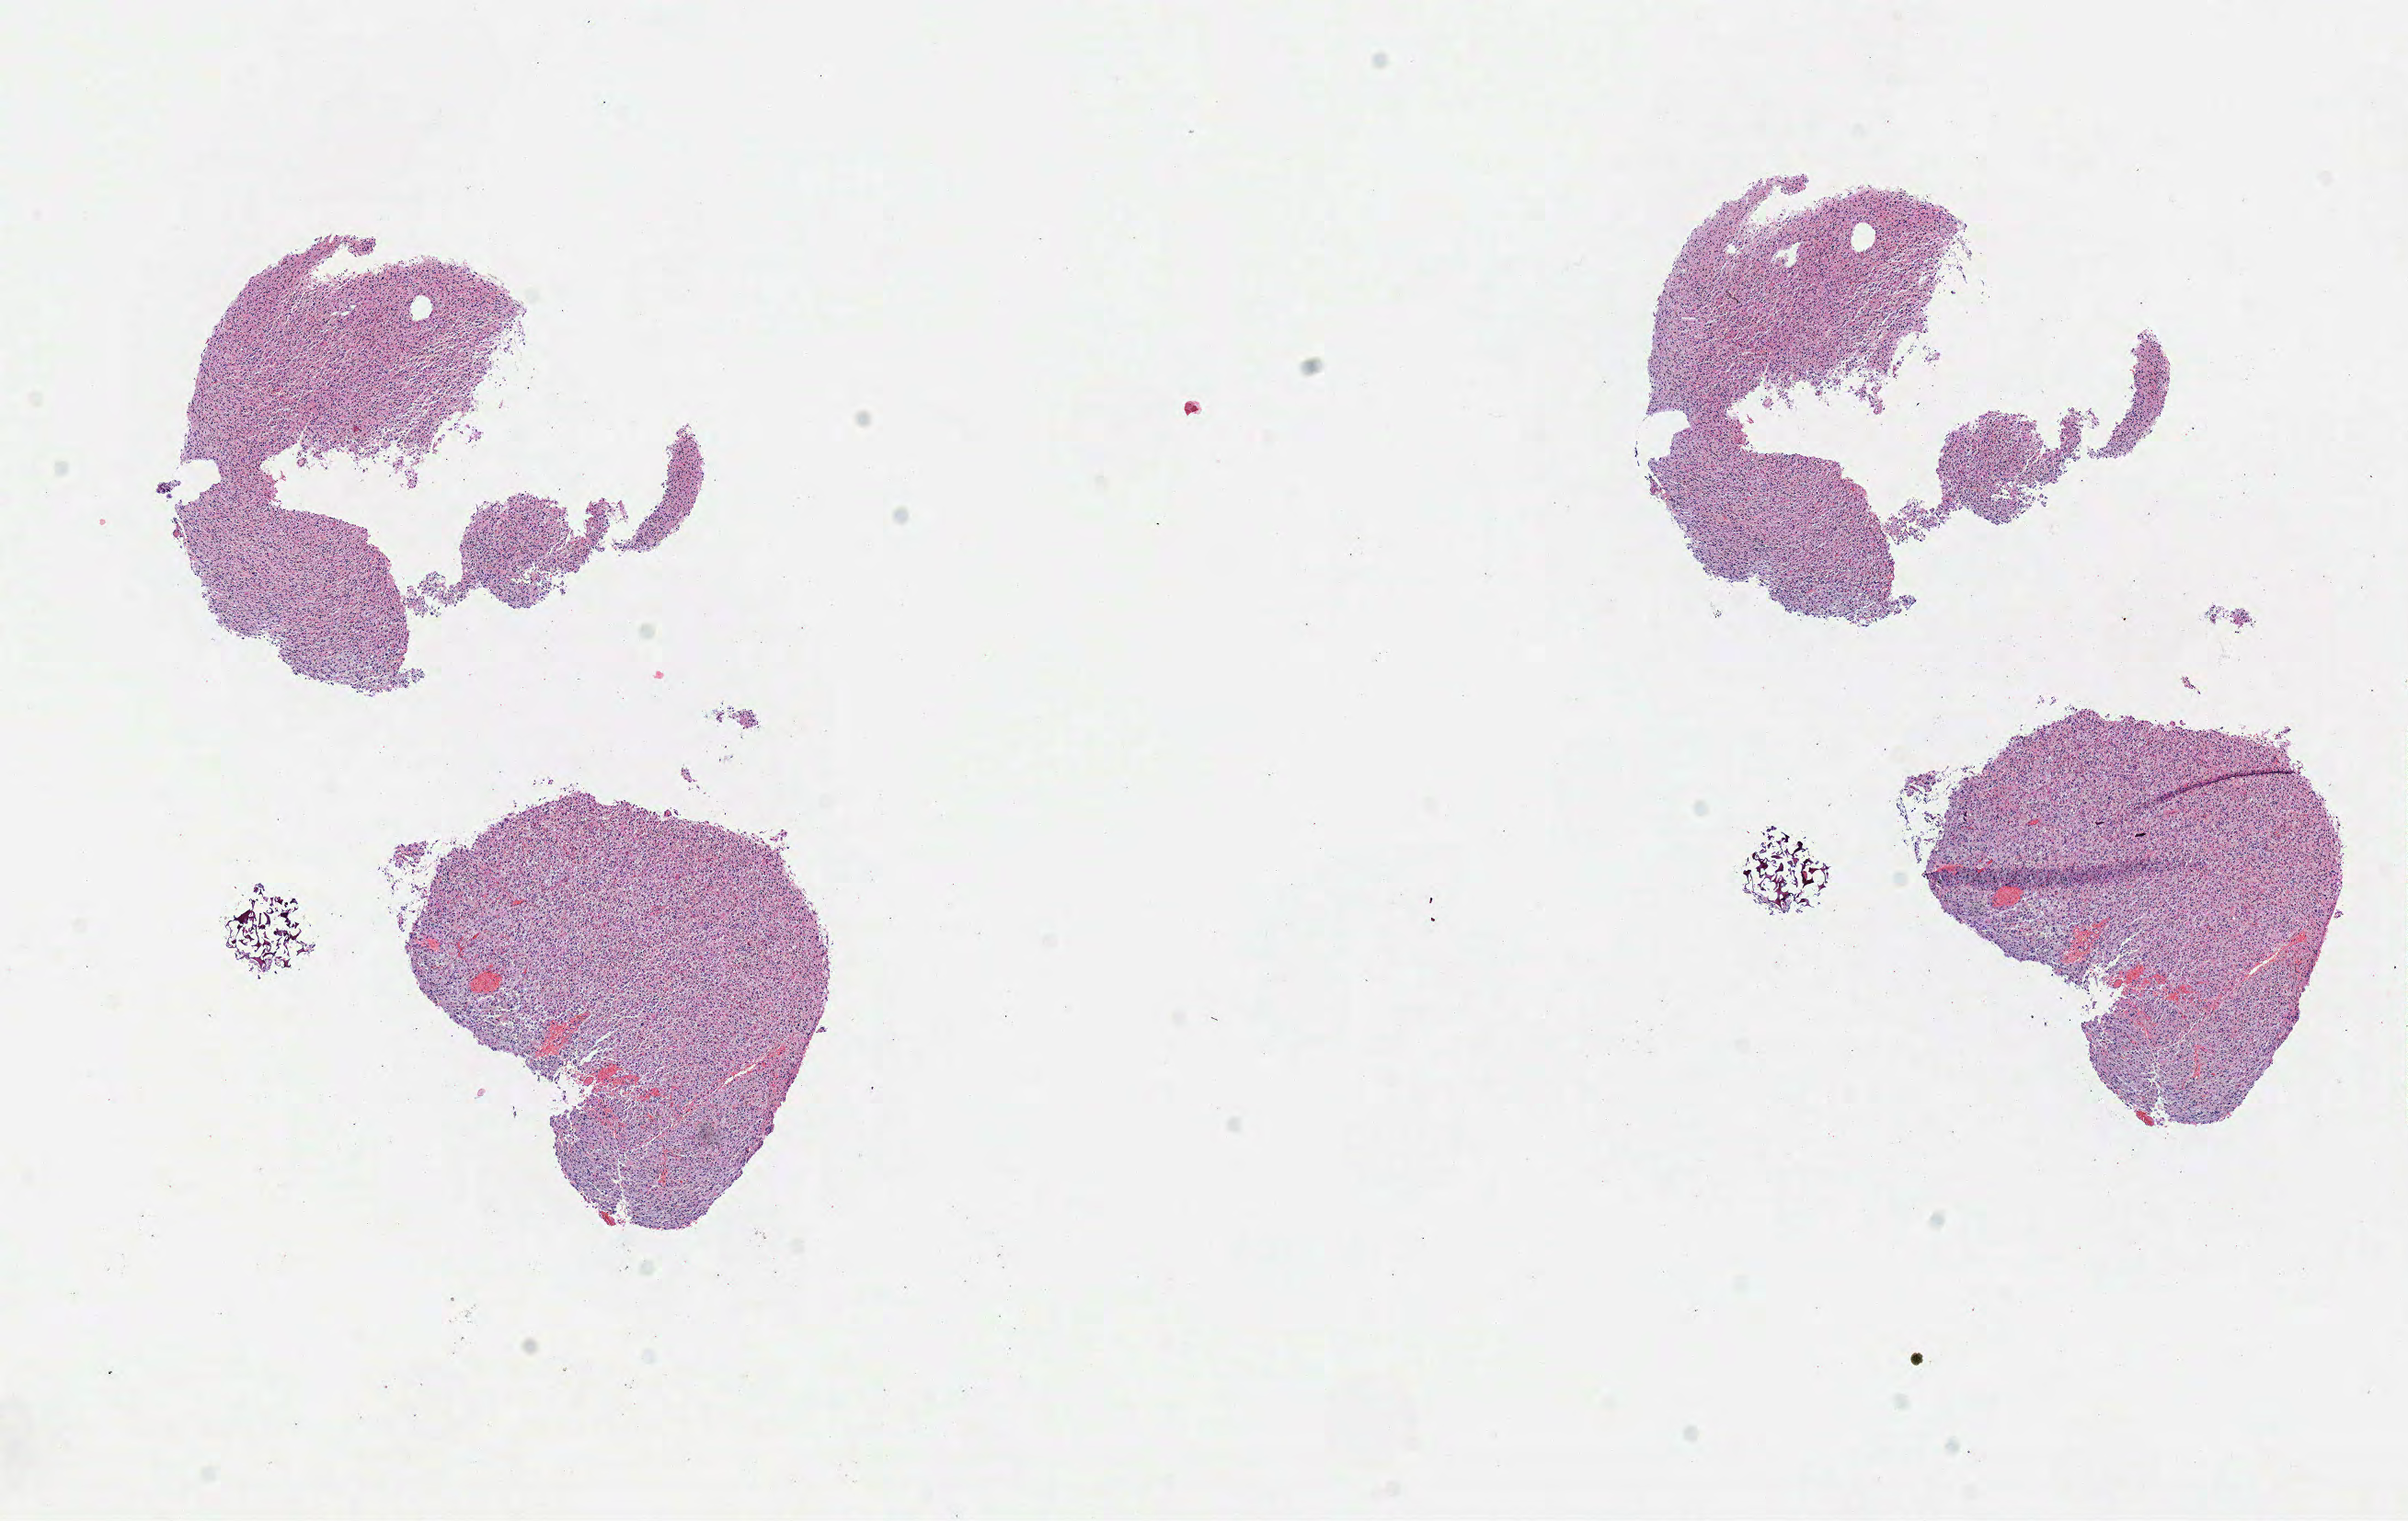
Digitized Hematoxylin and eosin (H&E) stained tissue section (whole slide), shown as a low-resolution overview of the whole scanned area (about 10.3 x 6.5 mm, from a 40x scan); frozen section from the top of the tissue portion; primary tumour sample from the brain. Female patient; age at initial diagnosis 40 years. Histologic grade: G3 (poorly differentiated). Composition of this section per pathologist review: tumour cells 100%, tumour nuclei 80%, normal cells 0%, stromal cells 0%, necrosis 0%.
Diagnosis: Mixed glioma.